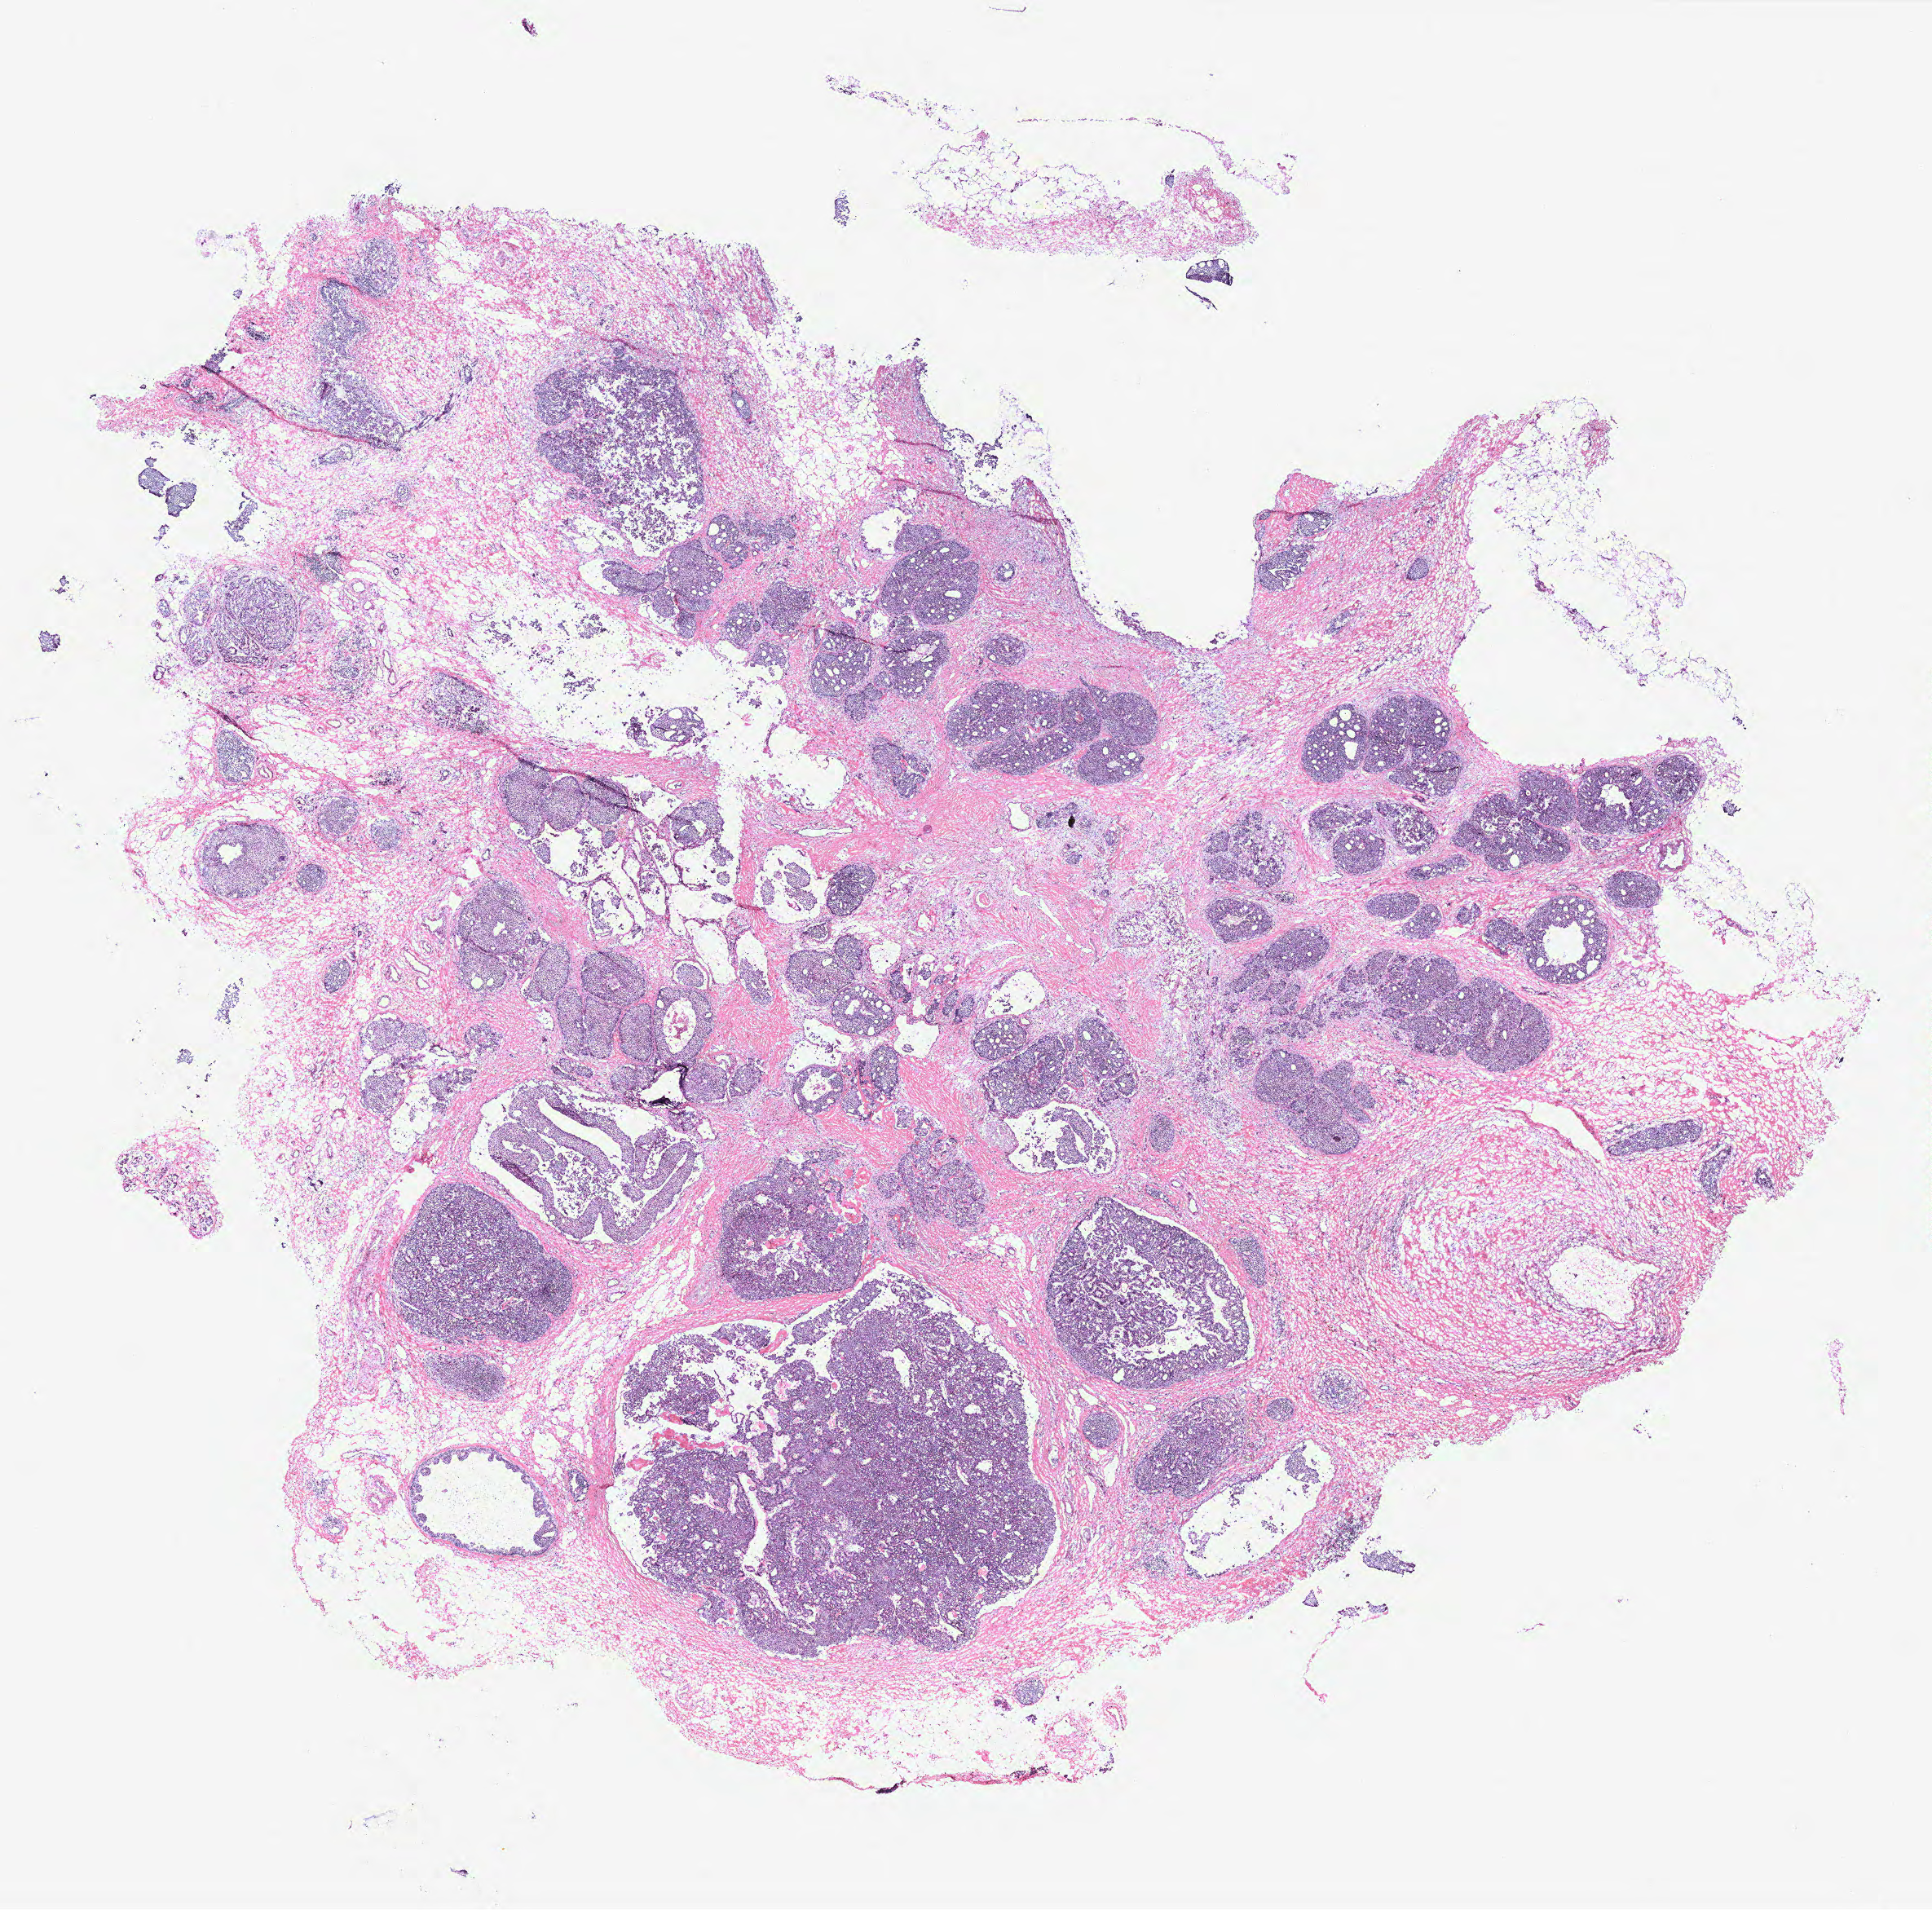
Whole-slide histology image, H&E-stained, shown as a low-resolution overview of the whole scanned area (about 19.0 x 18.8 mm, slide scanned at 40x). Breast, tissue type not recorded. Female, 67 y/o.
- patient diagnosis: Infiltrating duct carcinoma, NOS